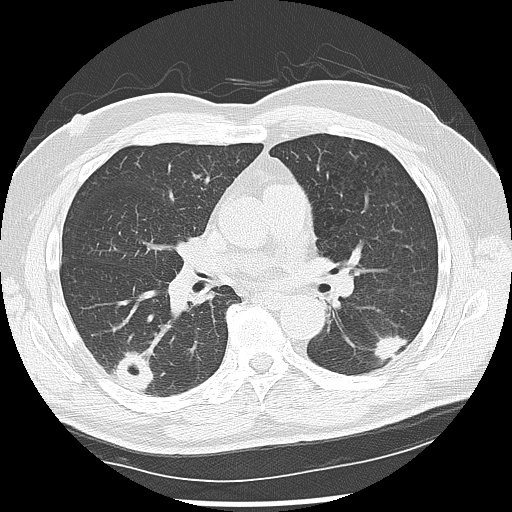
Low-dose screening chest CT, one axial slice. Slice 70 of 142 in the series (ordered by position). Reconstruction kernel LUNG. 120 kVp. Lung window (W 1500 / L -600 HU). 2.5 mm slice thickness. 512 × 512 image matrix.
Annotated regions visible in this slice (manually delineated by an expert):
- lesion 1 (nodule, lower lobe of left lung): bounding box (x1, y1, x2, y2) in pixels: (374, 335, 408, 362)
- lesion 2 (nodule, lower lobe of right lung): (111, 351, 154, 392)